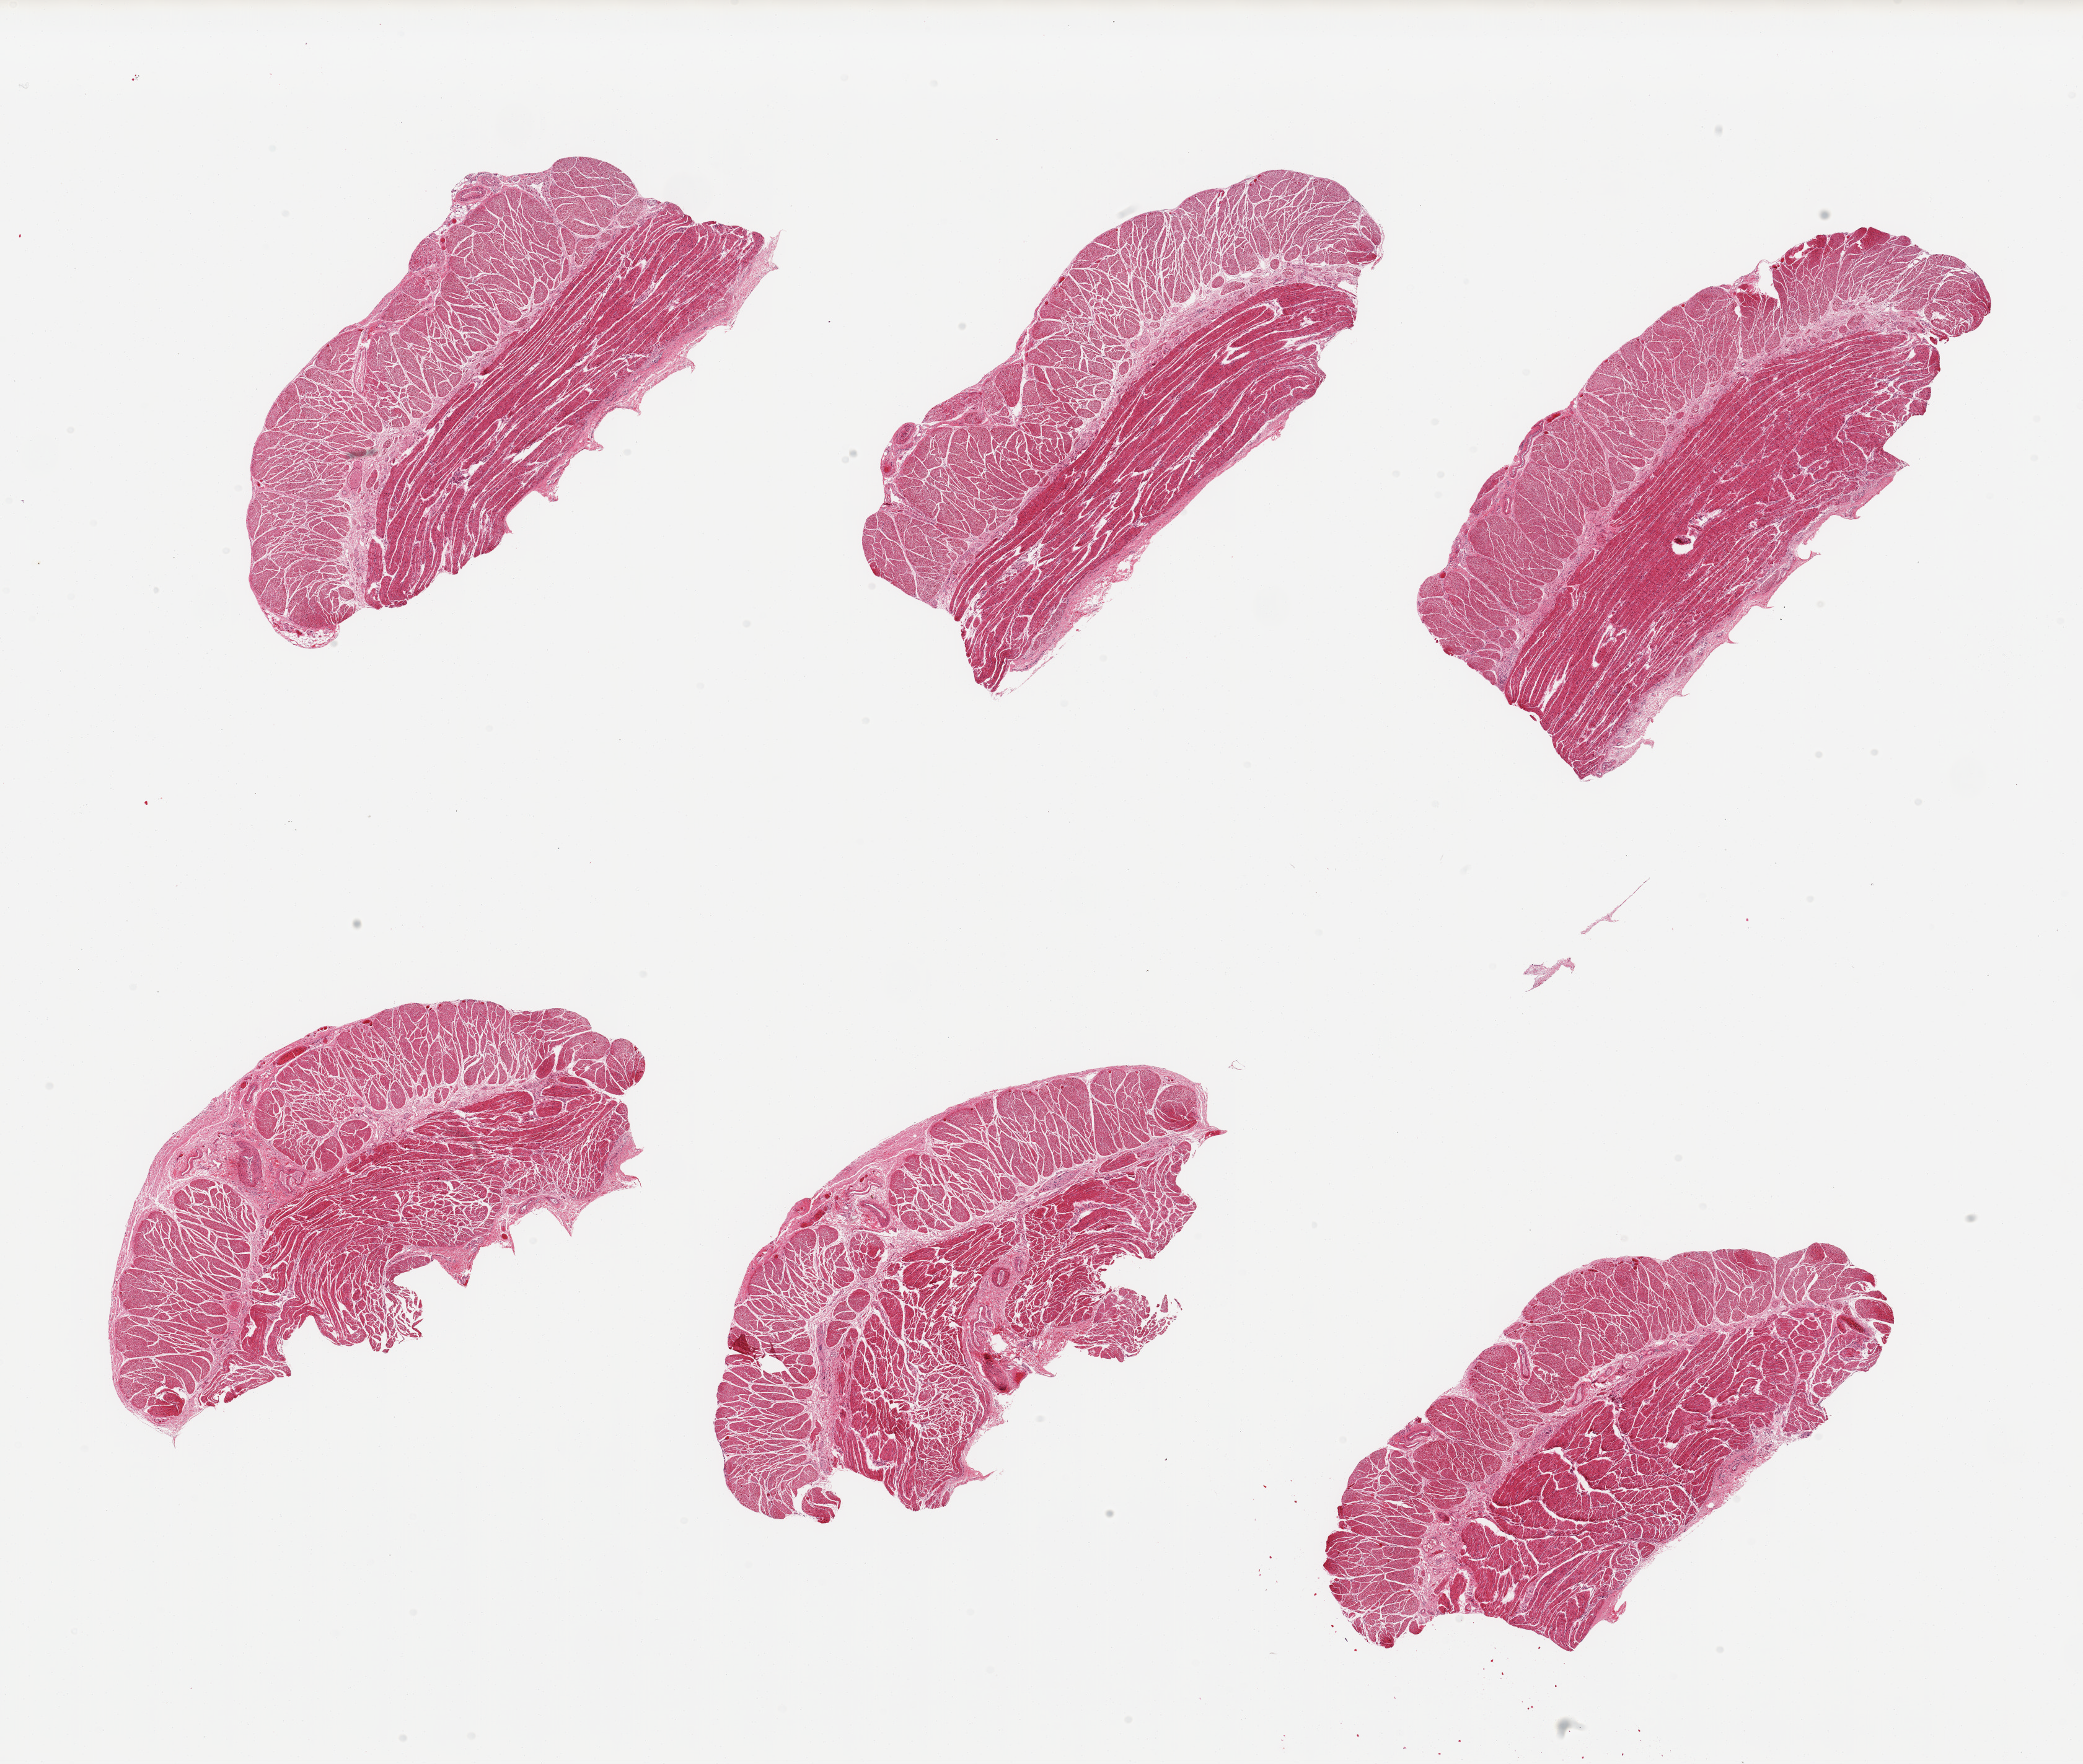
Hematoxylin and eosin (H&E) whole-slide image, shown as a low-resolution overview of the whole scanned area (about 26.6 x 22.5 mm, acquisition: 20x scan). PAXgene-fixed paraffin-embedded (PFPE) section. Target tissue: gastroesophageal junction. Donor tissue sample. Donor: male.
Review note (as recorded): 6 pieces confirmed target muscularis.